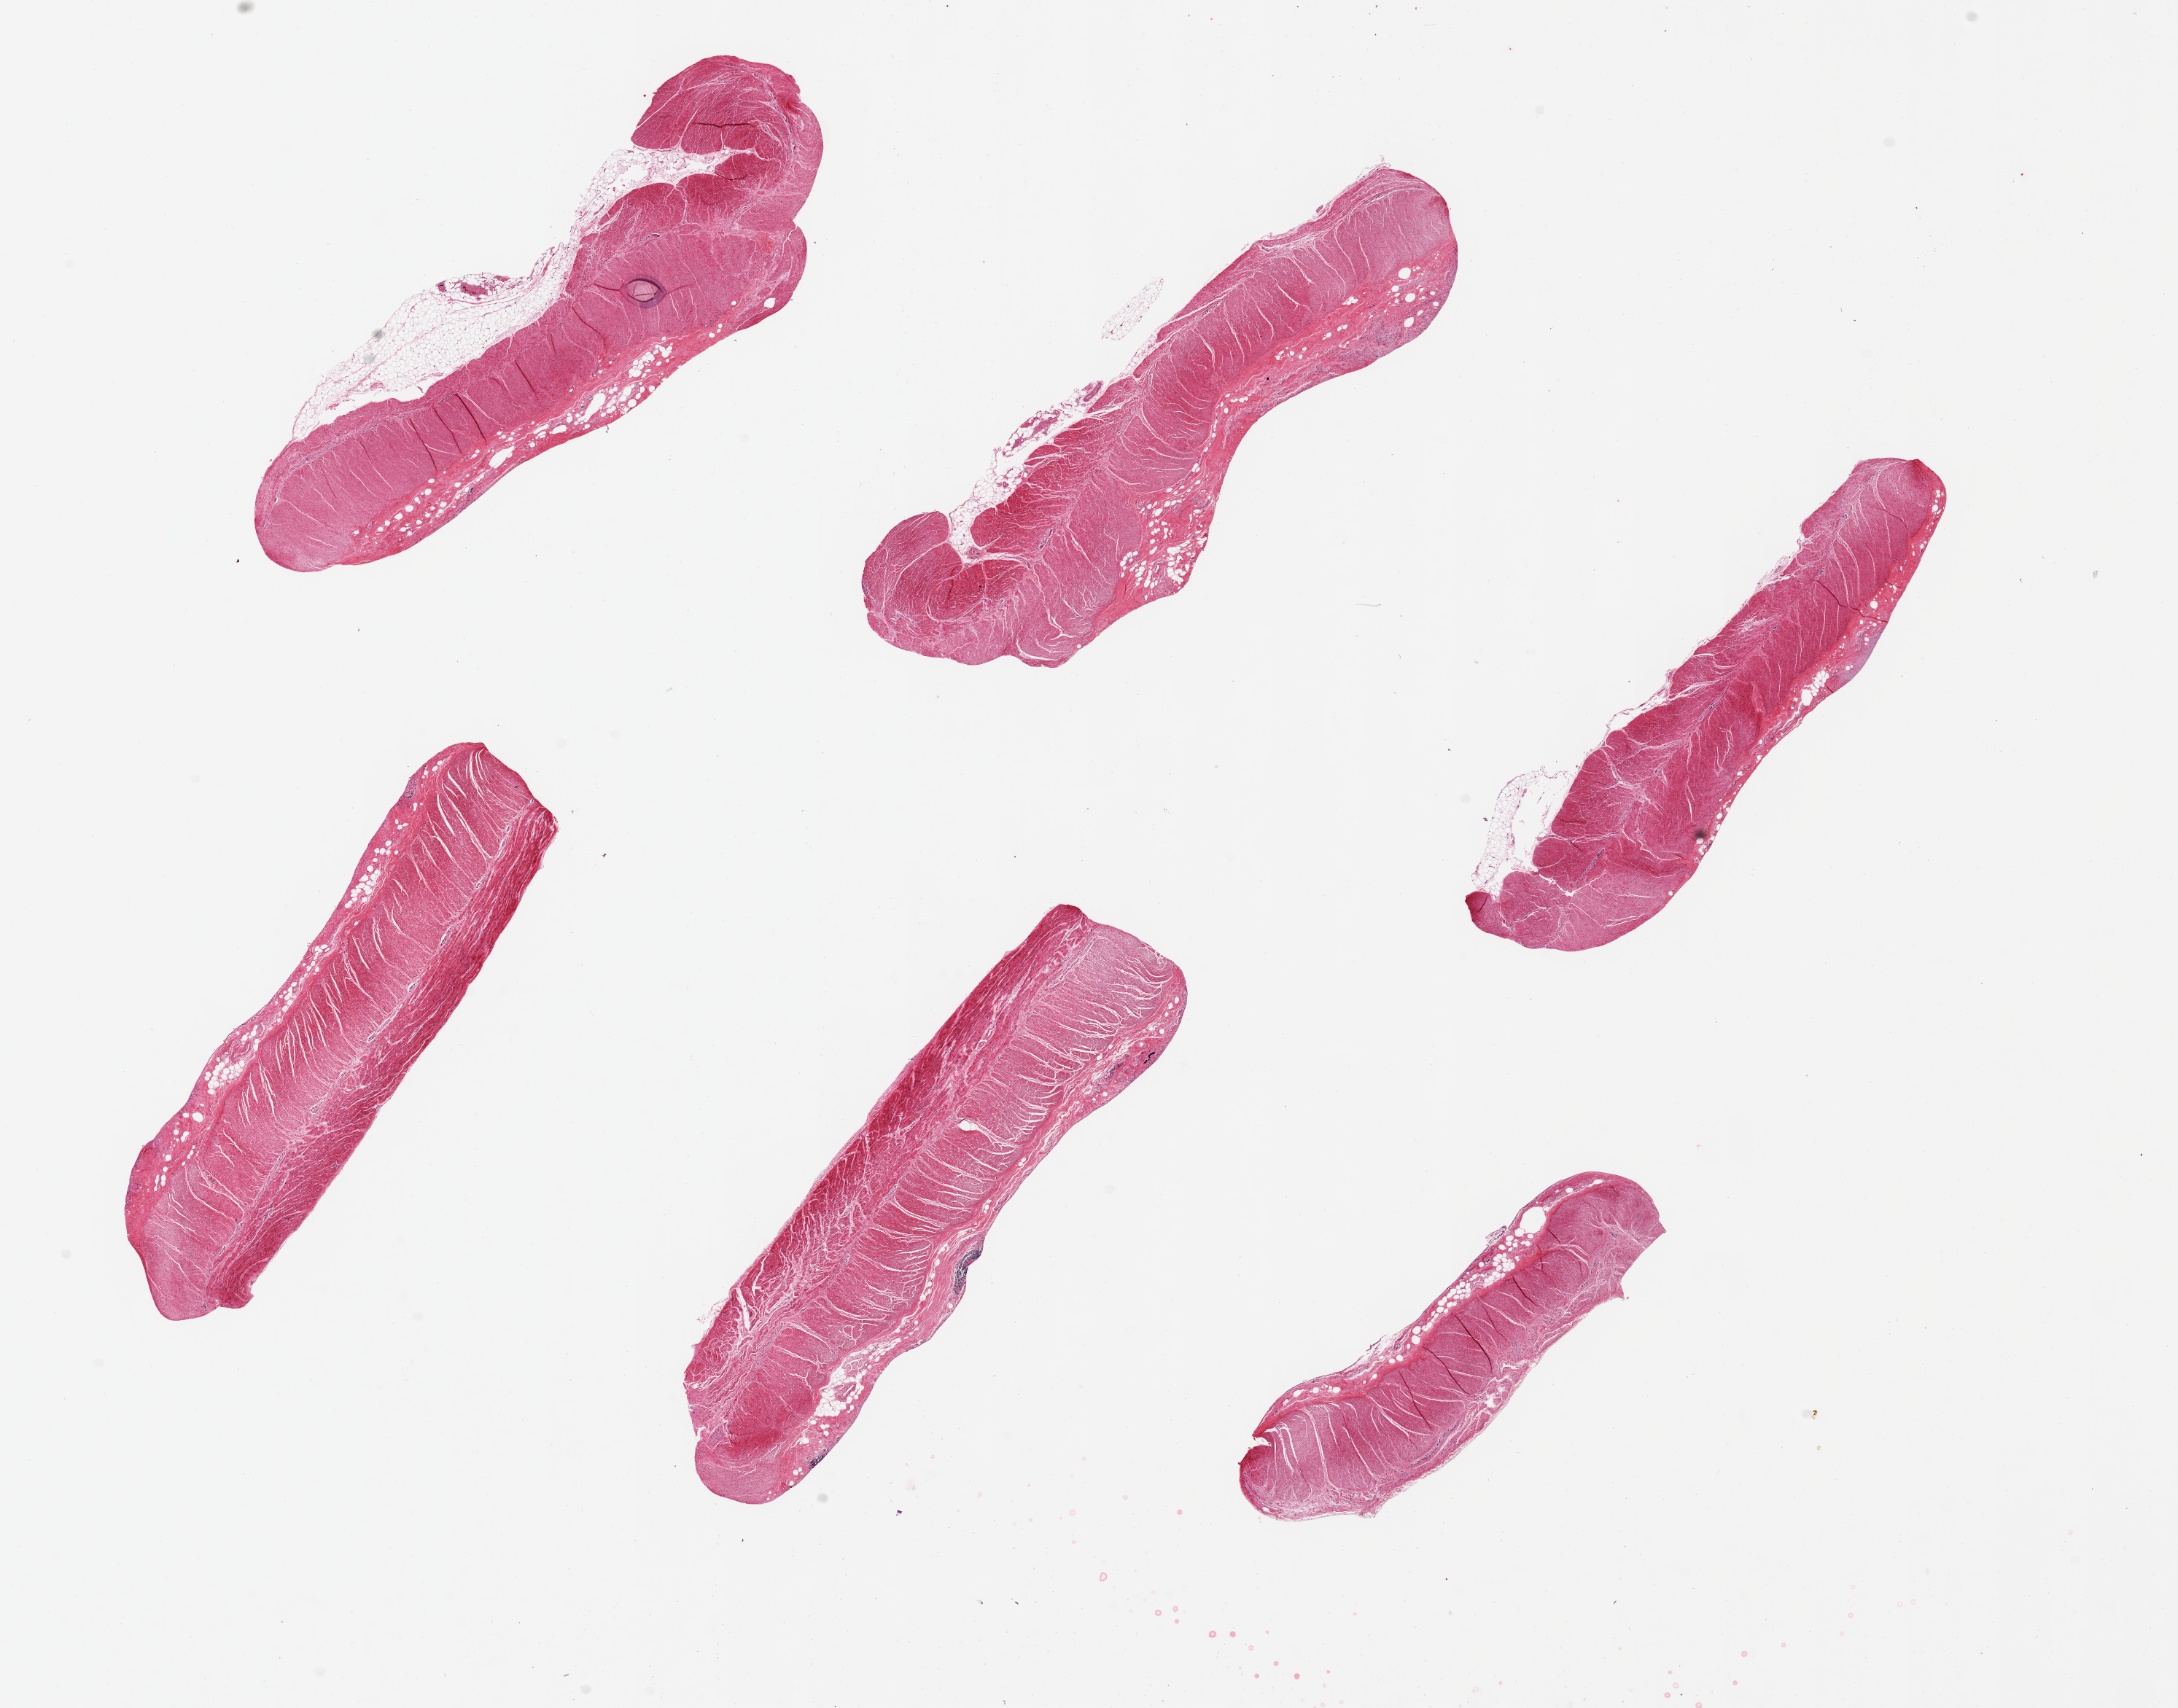
Whole-slide image, H&E stain — whole scanned area (about 23.6 x 18.5 mm, slide scanned at 20x) shown as a low-resolution overview; PAXgene-fixed, paraffin-embedded tissue; section of sigmoid colon (target tissue); donor tissue sample. Female donor.
Review note (as recorded): 6 pieces ~ 7x1.5mm, virtually all muscularis, clean speimens, but autolyzed.